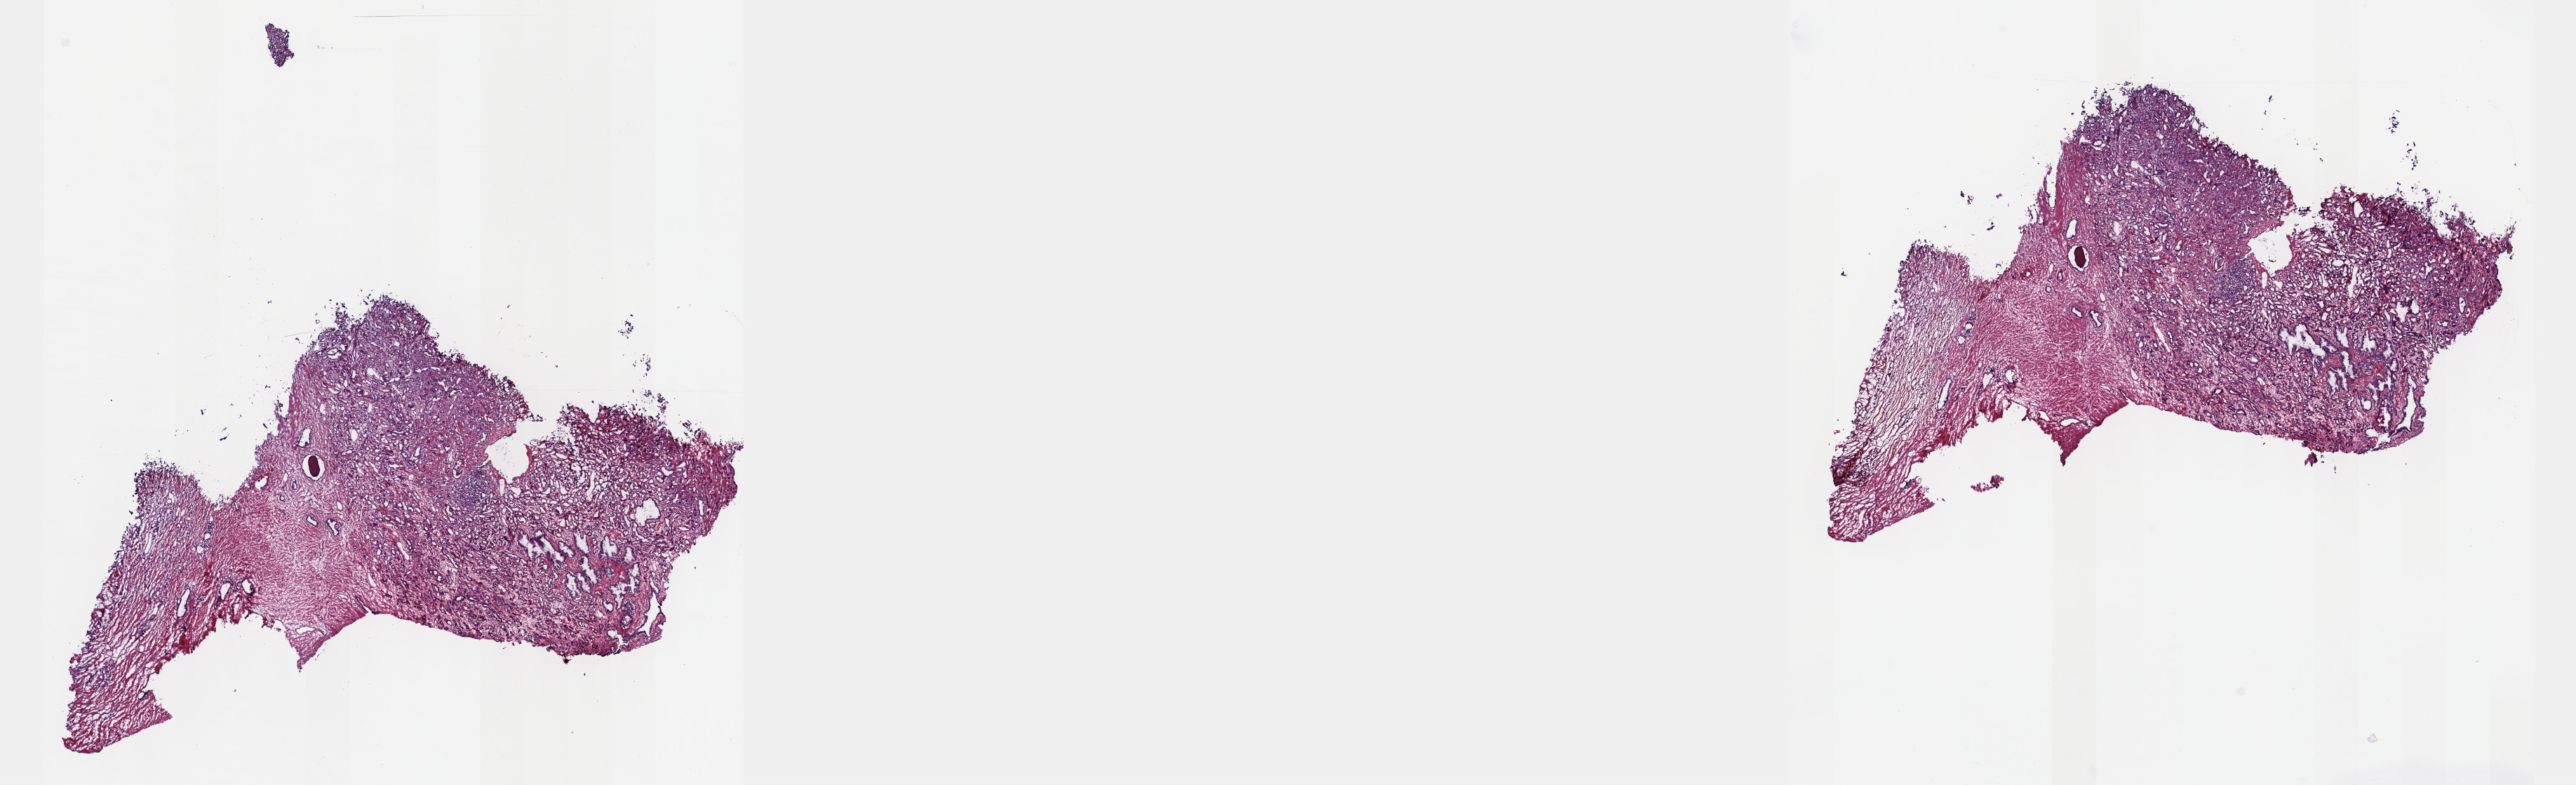
Digitized H&E tissue section (whole slide) — shown as a low-resolution overview of the whole scanned area (about 29.7 x 9.0 mm, from a 40x scan). Frozen section from the top of the tissue portion. Sample: primary tumour, prostate. Male patient; age at initial diagnosis 57 years. Gleason score: 7 (4+3). Pathologist review of this section (percent, as recorded): tumour cells 60%, tumour nuclei 70%, normal cells 10%, stromal cells 30%, necrosis 0%. Infiltration values recorded for this section: lymphocyte infiltration 0%, monocyte infiltration 0%, neutrophil infiltration 0%.
Pathologic diagnosis: Adenocarcinoma, NOS (prostate gland). Laterality: bilateral. Lymph nodes positive (case pathology): 1 of 13 examined.